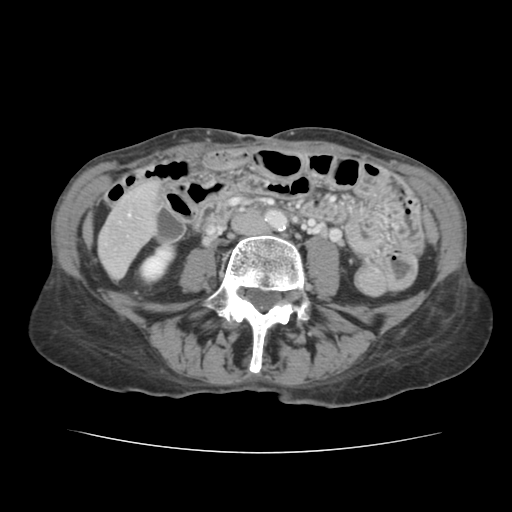
Contrast-enhanced abdominal CT, one axial slice. 120 kVp. Soft-tissue window (W 400 / L 40 HU). 512 × 512 image matrix. Female patient, age 77 years. Case-level facts recorded for this patient, not image findings: diagnosis: colorectal cancer liver metastases, imaged before liver resection; multiple liver metastases: yes; largest metastasis: 3 cm; disease in both lobes: no.
Structures marked on this image (manually delineated by an expert):
- liver: bounding box (x1, y1, x2, y2) in pixels: (100, 185, 158, 277)